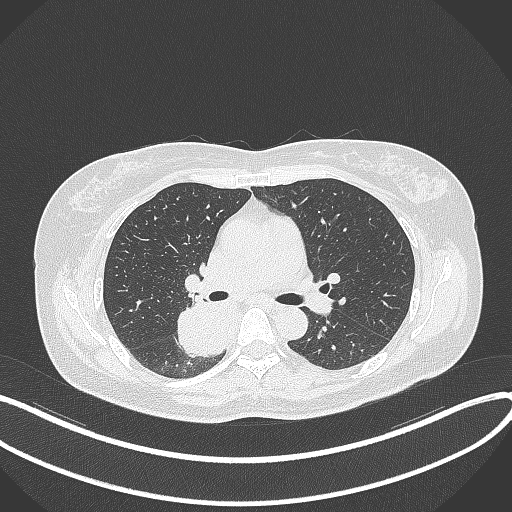
Chest CT, one axial slice. Slice 217 of 331 in the series (ordered by position). 120 kVp. Lung window (W 1500 / L -600 HU). 512 × 512 image matrix. Patient: female, 54 years. From the clinical record (not read from this slice): clinical TNM (as recorded): T4 N0 M0.
Outlined on this slice (bounding box drawn by a radiologist):
- lung tumour (recorded histology: adenocarcinoma): box from (x=175, y=296) to (x=231, y=358) px